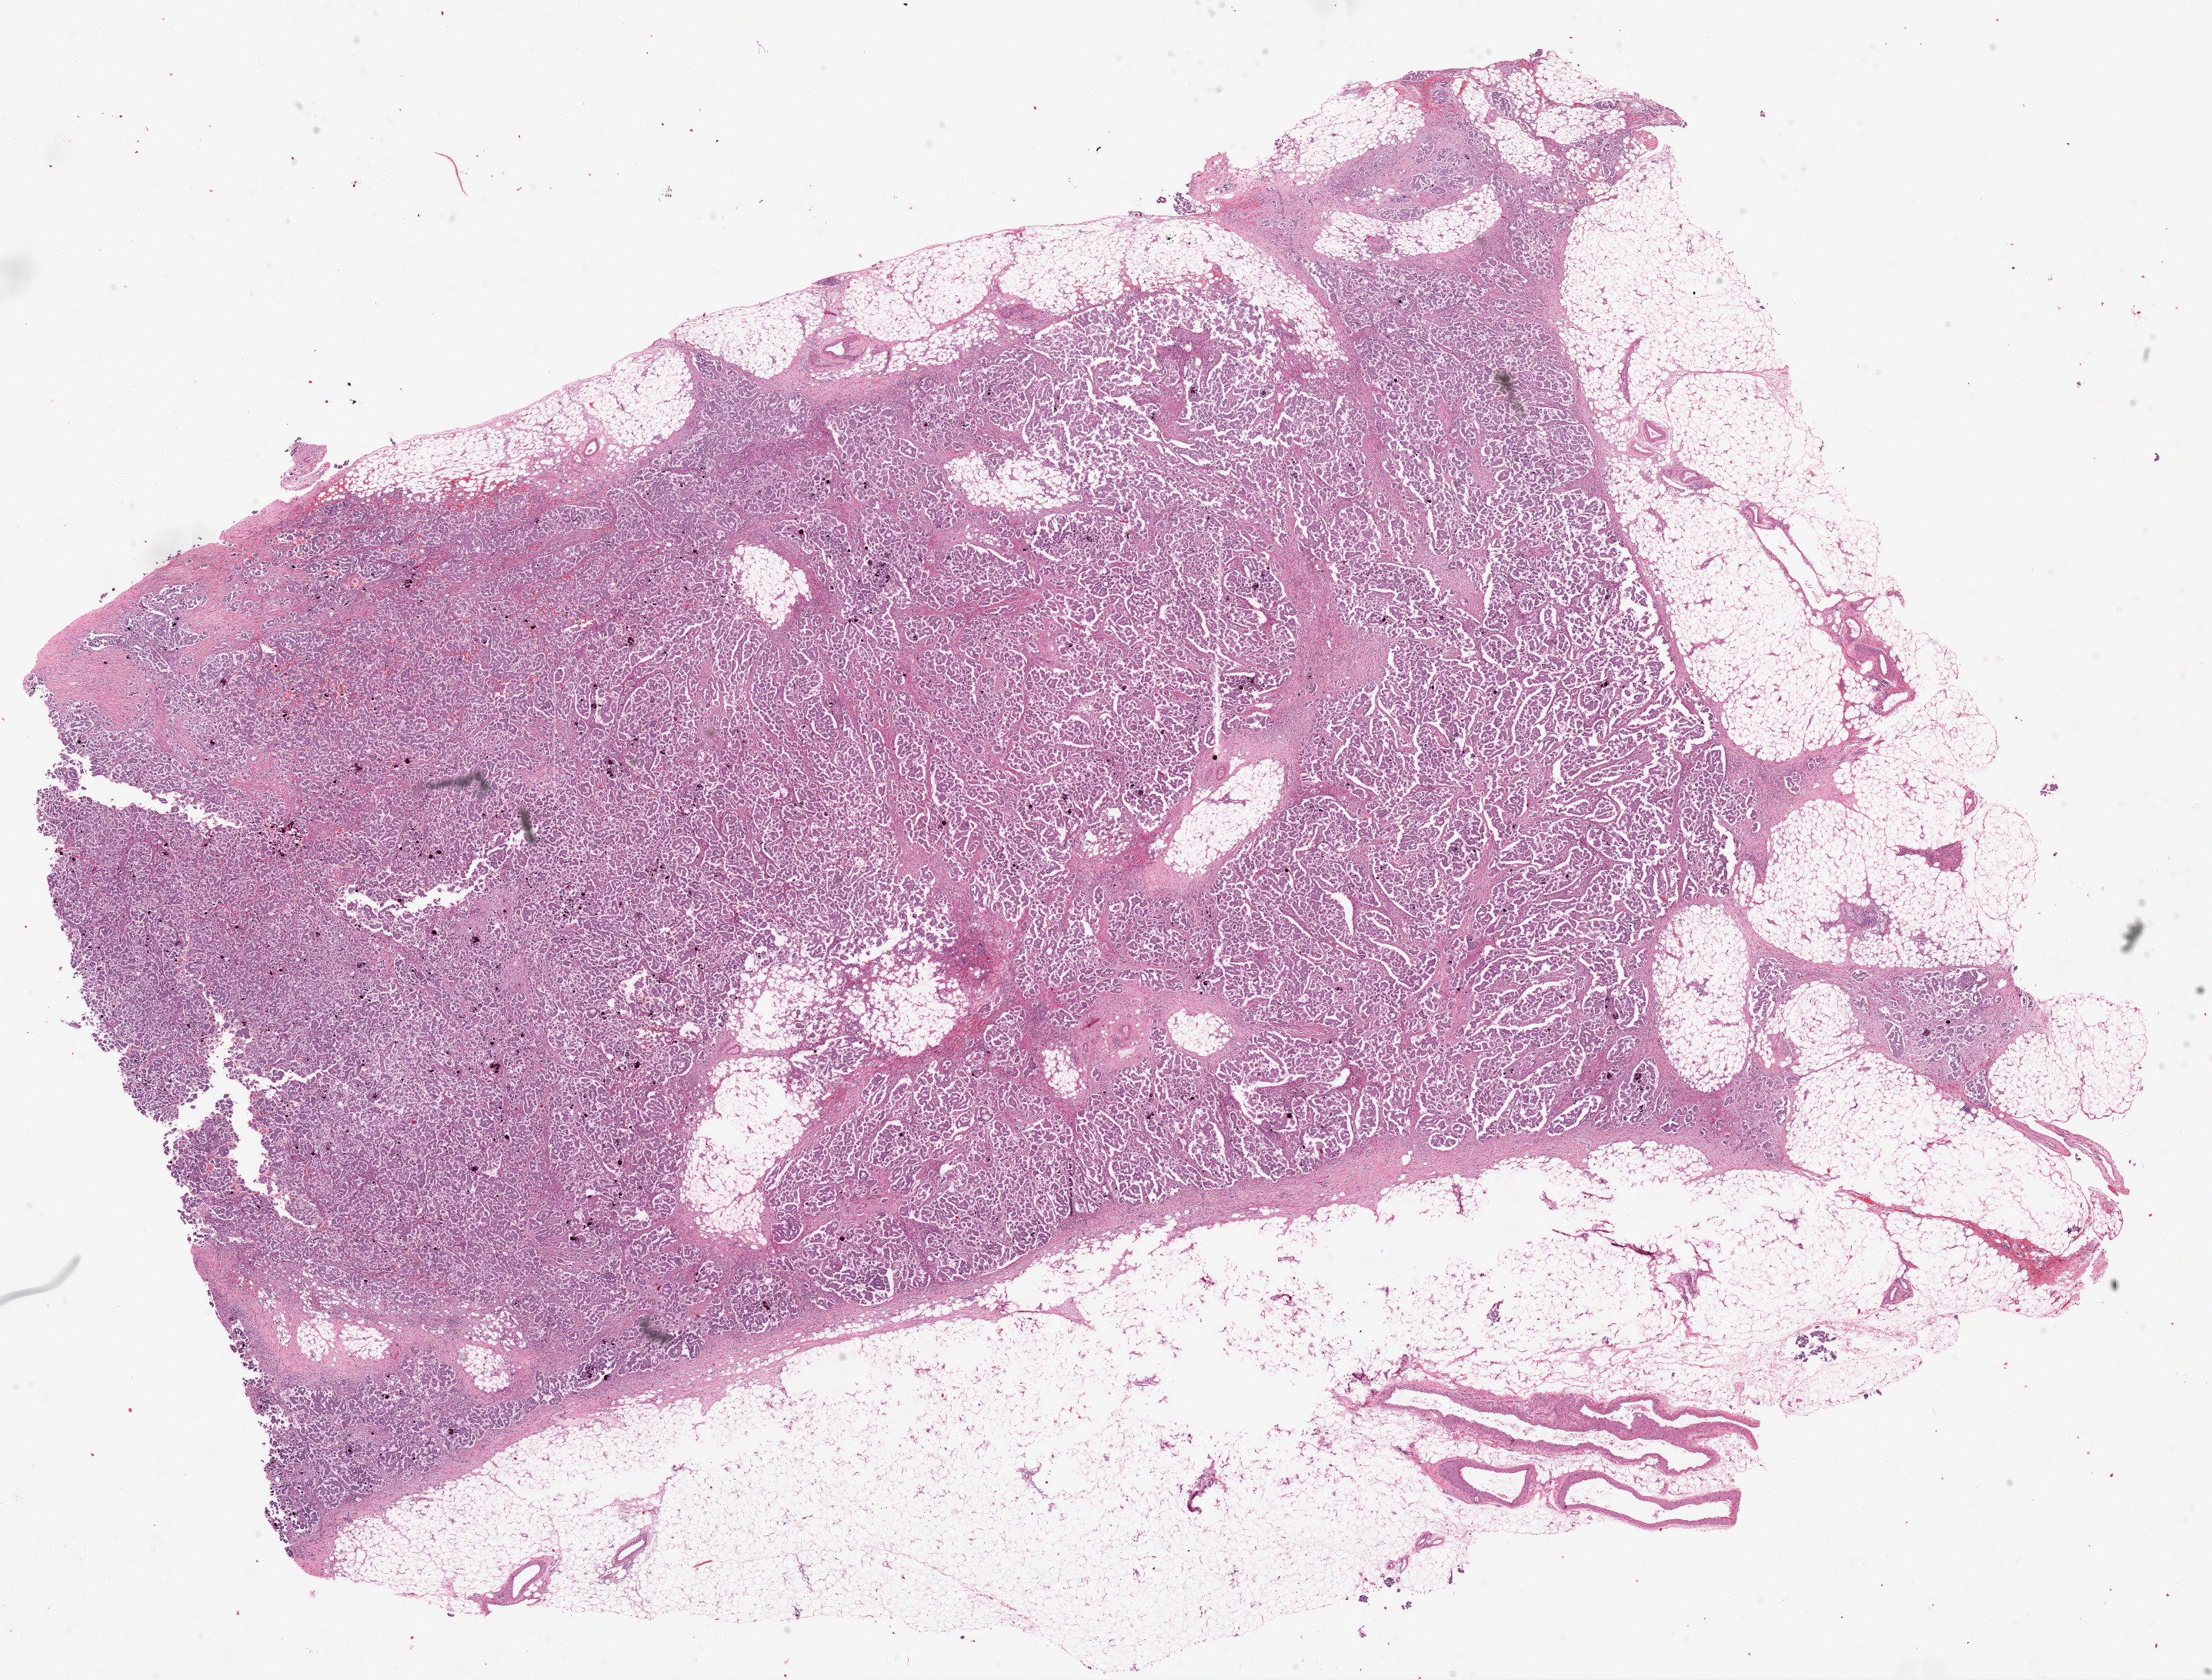
Digitized H&E tissue section (whole slide), low-resolution overview of the scanned area, about 23.1 x 17.5 mm (slide scanned at 20x); frozen section from the top of the tissue portion; primary tumour sample from the ovary. Female patient; age at initial diagnosis 26 years. Histologic grade: G1 (well differentiated). Pathologist review of this section (percent, as recorded): tumour cells 82%, tumour nuclei 80%, normal cells 20%, stromal cells 8%, necrosis 0%.
Laterality: bilateral. Pathologic diagnosis: Serous cystadenocarcinoma, NOS. FIGO stage: IIIC.